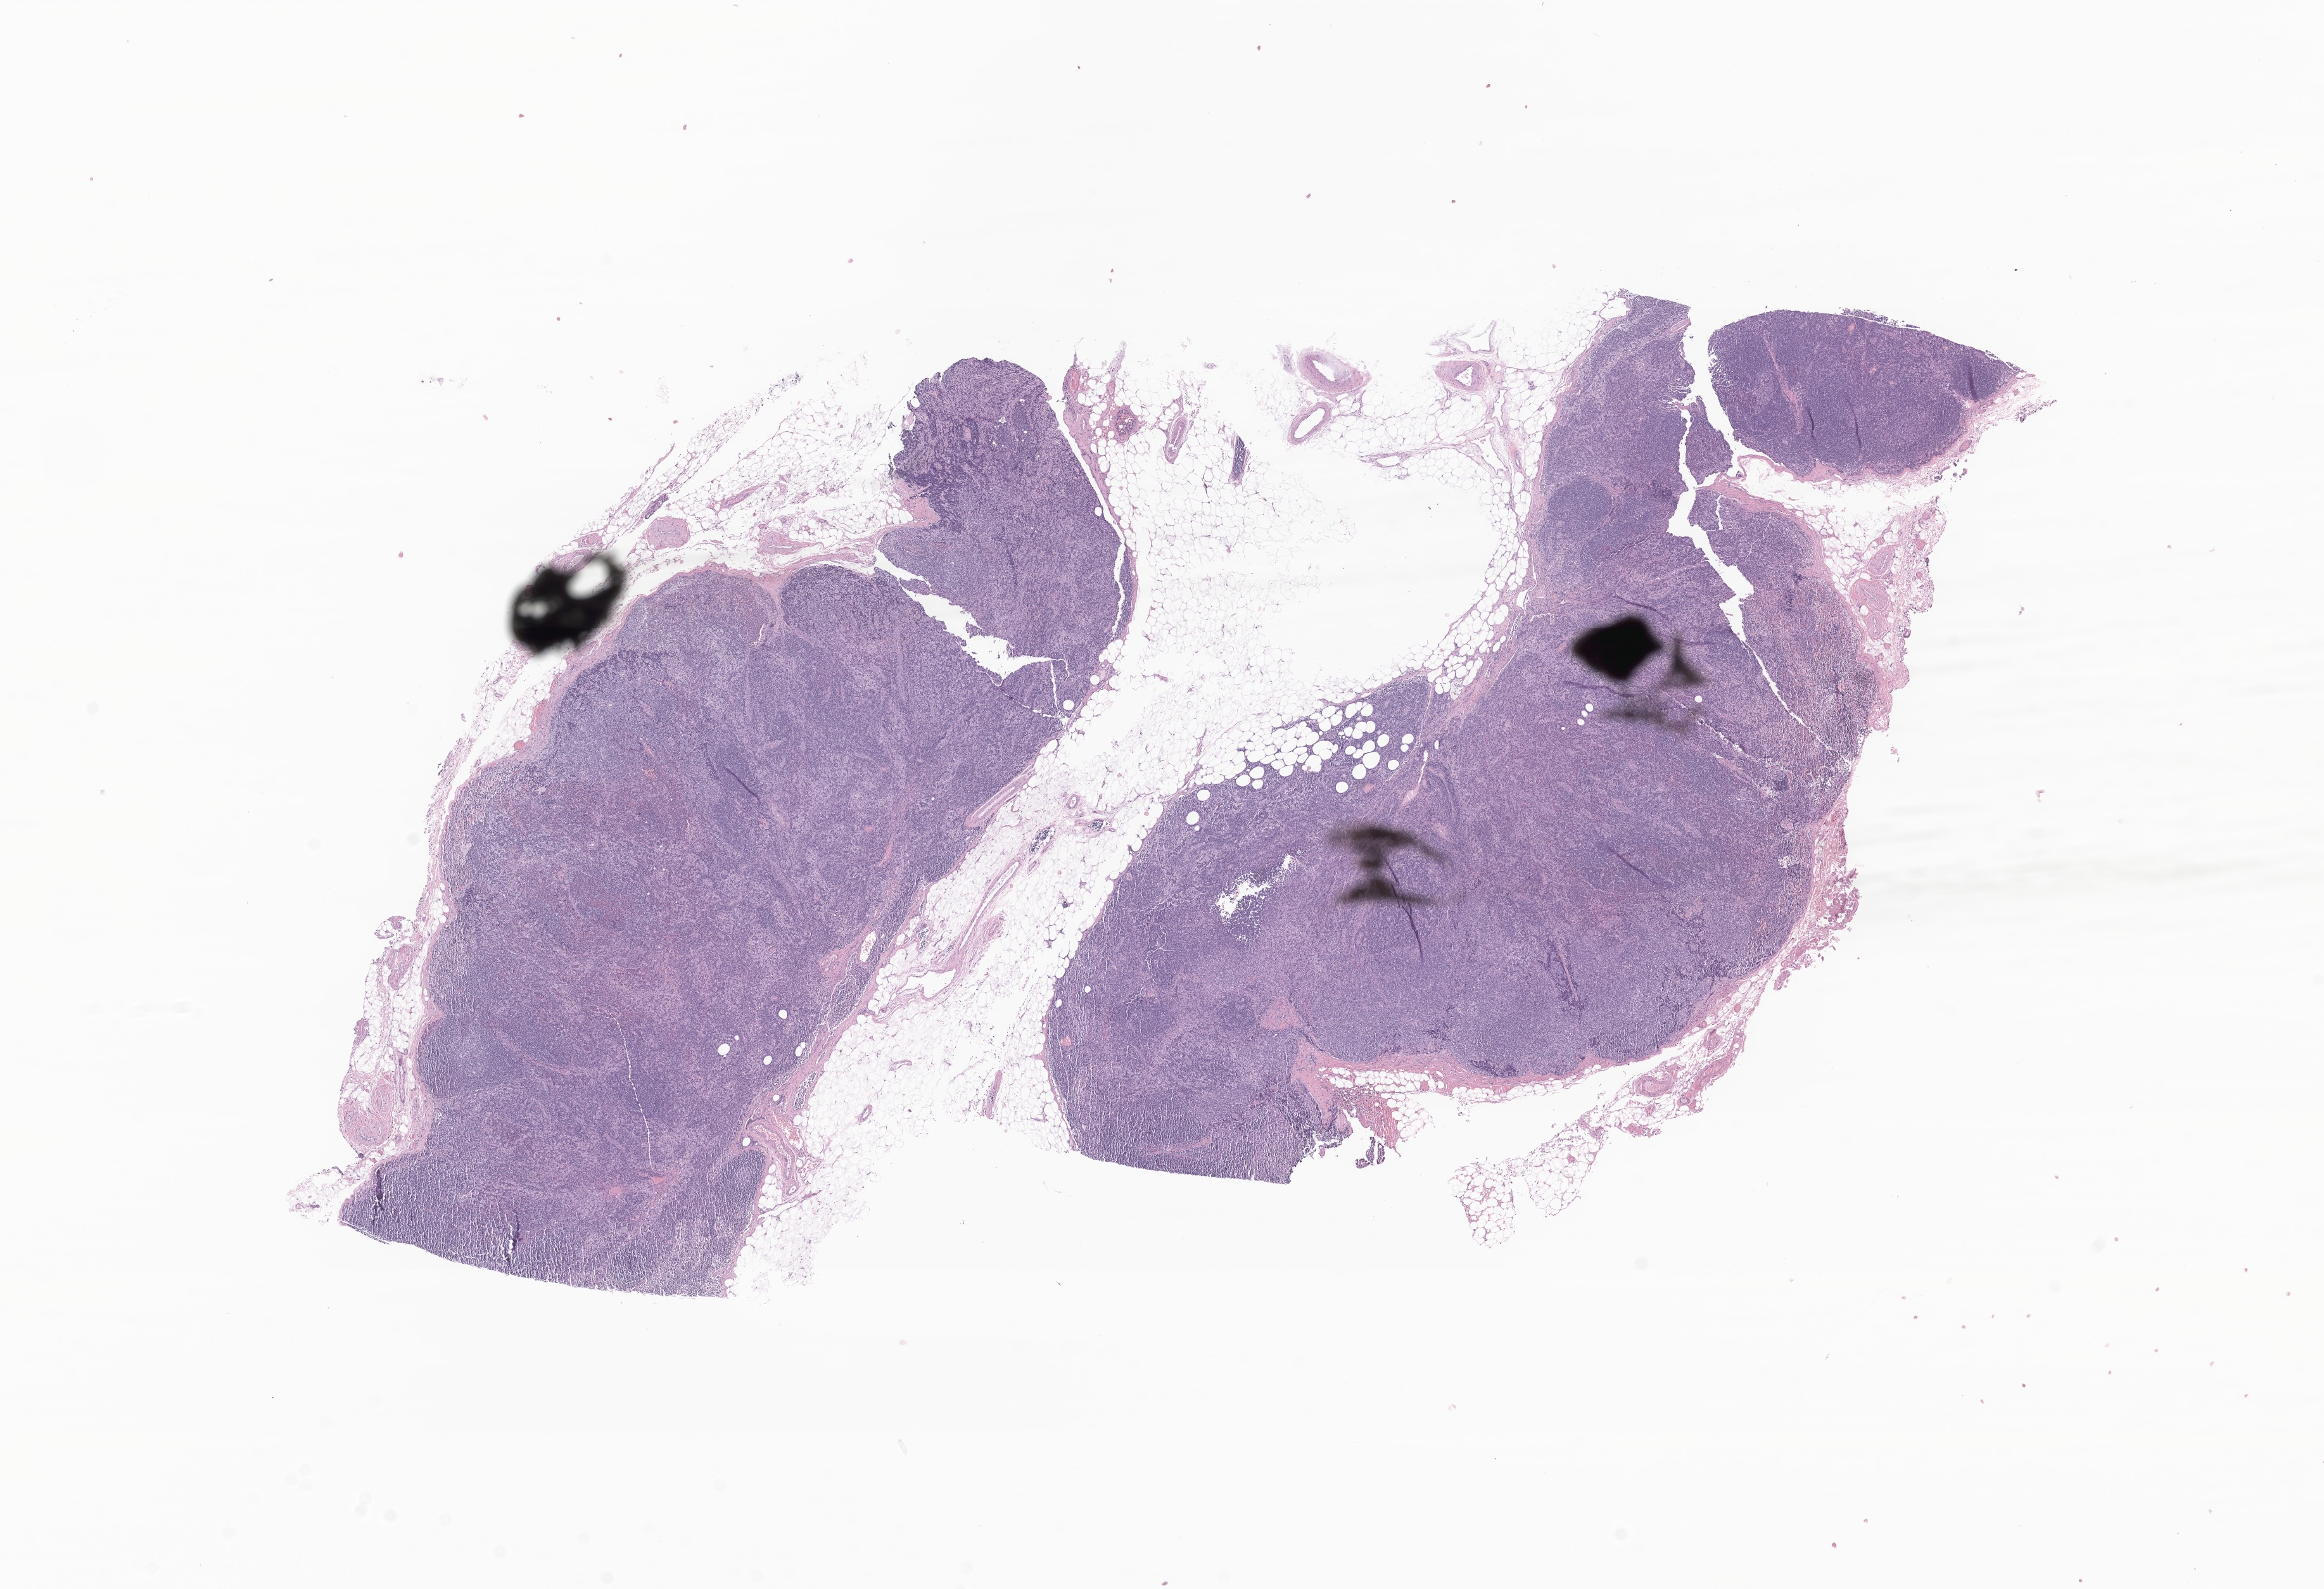
Hematoxylin and eosin (H&E) whole-slide image of tumor tissue from the upper limb — shown as a low-resolution overview of the whole scanned area (about 15.5 x 10.6 mm), formalin-fixed paraffin-embedded section. Male patient, age 178 months.
* diagnosis (ICD-O-3 morphology term): Sarcoma, NOS